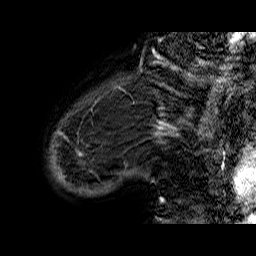
Breast MRI (dynamic contrast-enhanced), one sagittal slice. Slice 5 of 60 in the series (ordered by position). Dynamic contrast-enhanced series, time point 2 of 6 at this slice position (early post-contrast). 1.5 T. TE 6.5 ms, TR 32.9 ms. 4 mm slice thickness. 256 × 256 image matrix, field of view 200 × 200 mm. Female patient. Case-level facts recorded for this patient, not image findings: setting: breast cancer imaged before/during neoadjuvant chemotherapy; receptor status: HR-positive, HER2-negative.
Annotated regions visible in this slice (semi-automatic segmentation, software-assisted and operator-edited):
- analysis volume of interest (the breast-tissue region the enhancement analysis was run in; not a lesion): bounding box [x1, y1, x2, y2] px = [49, 74, 176, 209]
- tumour enhancement mask (voxels above the 100 % enhancement threshold inside the analysis volume of interest): [80, 122, 165, 203]